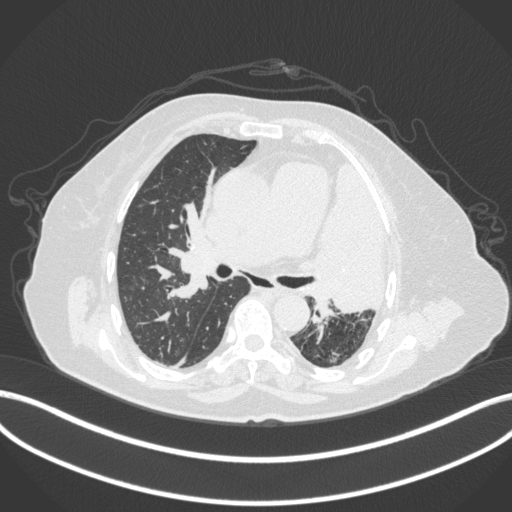
Chest CT, one axial slice. Slice 228 of 399 in the series (ordered by position). Reconstruction kernel B31f. Lung window (W 1500 / L -600 HU). 512 × 512 image matrix, field of view 400 × 400 mm. Patient: female, 75 years. Case-level facts recorded for this patient, not image findings: clinical TNM (as recorded): T3 N3 M1.
Outlined on this slice (bounding box drawn by a radiologist):
- lung tumour (recorded histology: adenocarcinoma): bounding box [x1, y1, x2, y2] px = [309, 160, 386, 317]